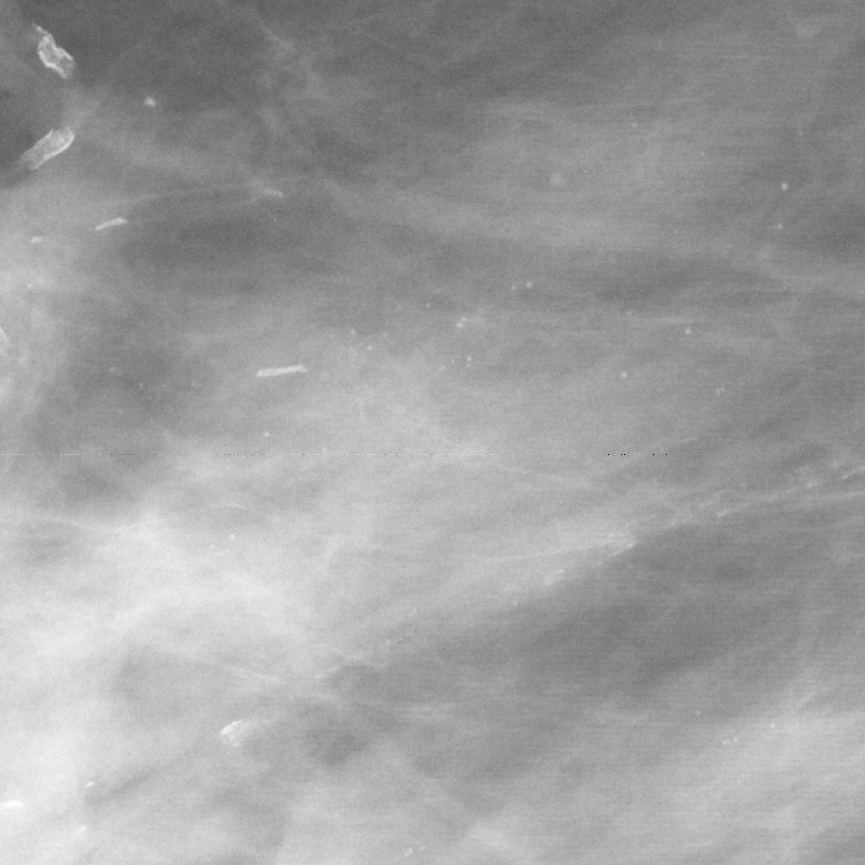
Region of interest cut from a scanned film mammogram (one marked finding), right breast, MLO view, BI-RADS breast density category 2 (scale 1–4).
Marked abnormality: calcifications, morphology punctate, distribution segmental; BI-RADS assessment category 4; pathology result (as recorded, not read from the image): benign.